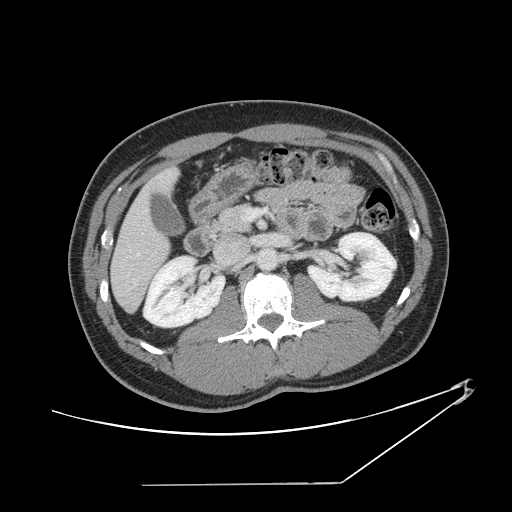
Contrast-enhanced abdominal CT, one axial slice. Slice 61 of 152 in the series (ordered by position). Intravenous contrast given. Soft-tissue window (W 400 / L 40 HU). 2.5 mm slice thickness. 512 × 512 image matrix. Male patient, age 45 years. Case-level facts recorded for this patient, not image findings: diagnosis: colorectal cancer liver metastases, imaged before liver resection; multiple liver metastases: no; largest metastasis: 1 cm; chemotherapy before resection: yes.
Outlined on this slice (expert manual segmentation):
- hepatic veins: bounding box [x1, y1, x2, y2] px = [127, 251, 140, 258]
- liver: [112, 172, 176, 311]
- planned liver remnant (the part of the liver to remain after resection): [112, 171, 176, 311]
- portal vein (with intrahepatic branches): [246, 210, 266, 220]